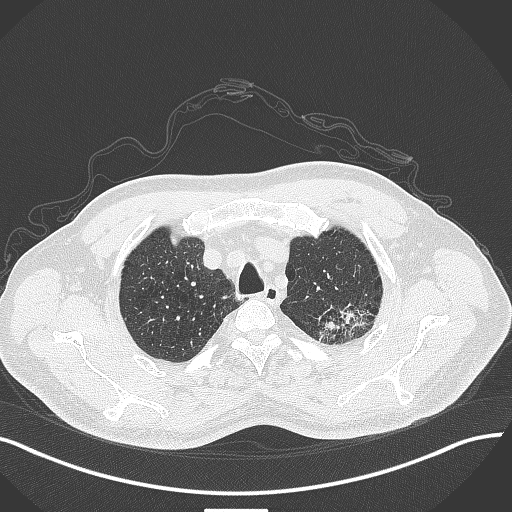
Chest CT, one axial slice. Reconstruction kernel B70f. Lung window (W 1500 / L -600 HU). 1 mm slice thickness. 512 × 512 image matrix. Patient: male, 55 years. Case-level facts recorded for this patient, not image findings: clinical TNM (as recorded): T3 N0 M1c.
Structures marked on this image (bounding box drawn by a radiologist):
- lung tumour (recorded histology: adenocarcinoma): box from (x=312, y=300) to (x=387, y=346) px